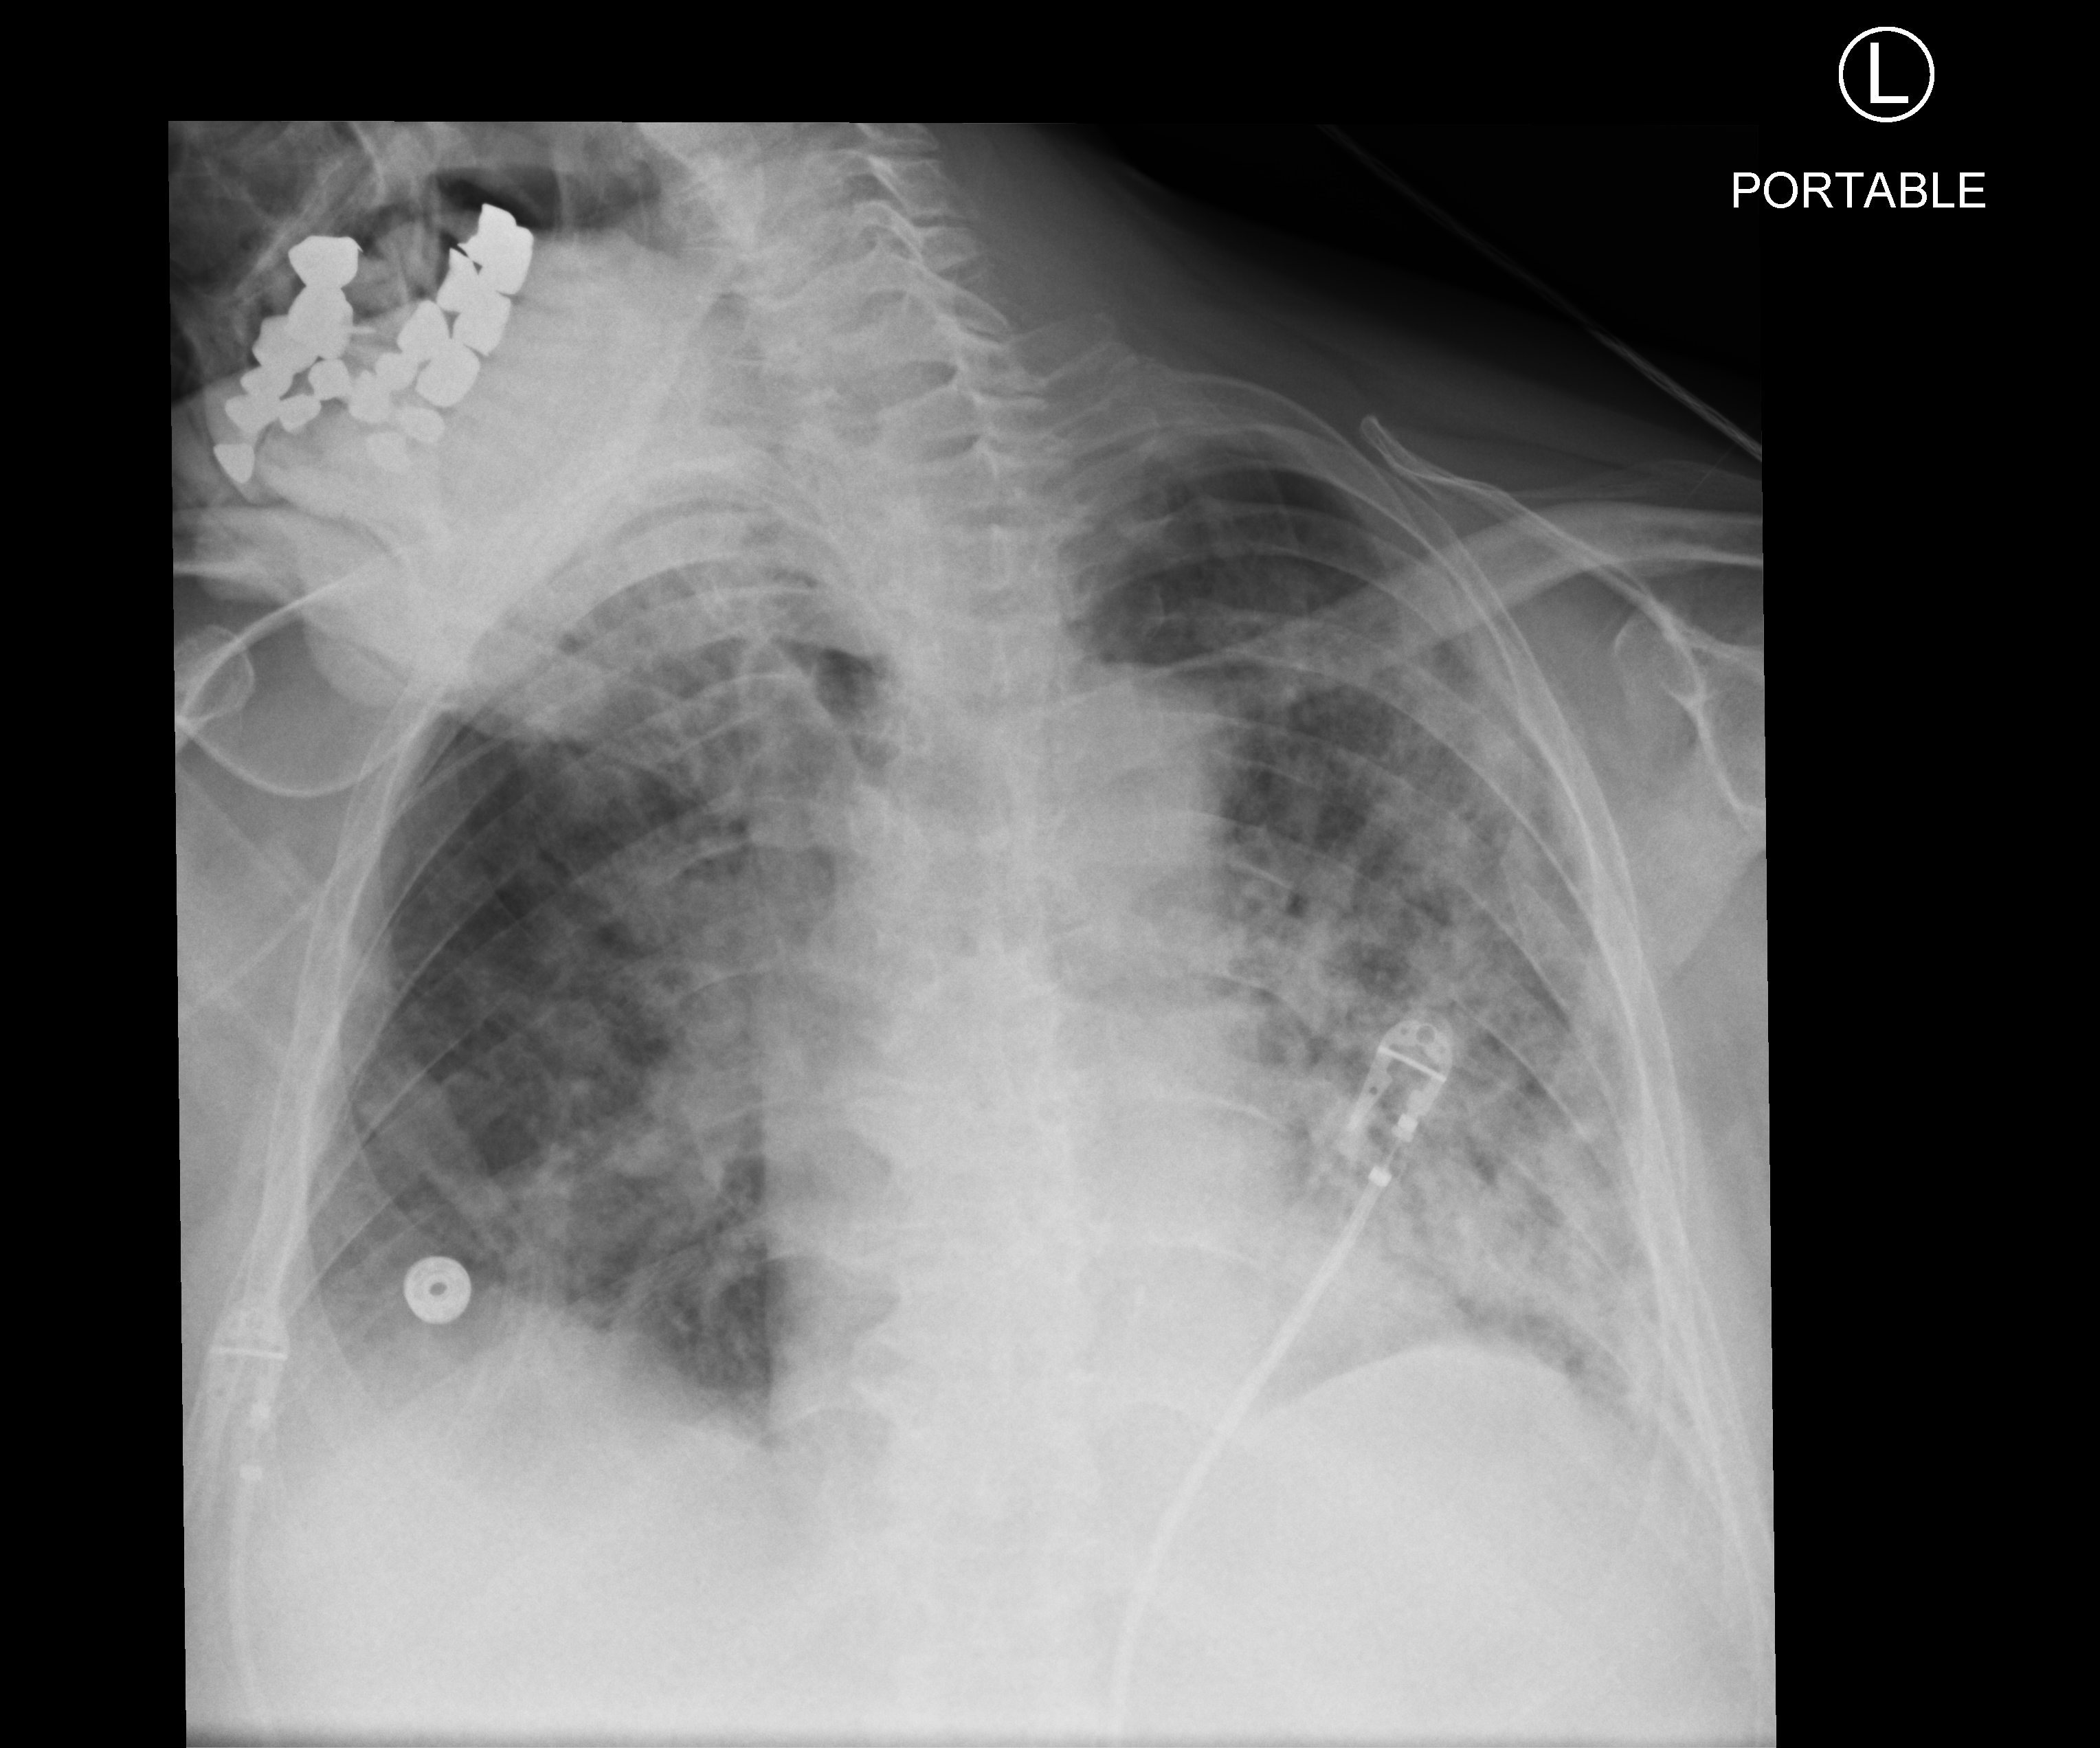
Bedside chest radiograph (computed radiography); anteroposterior (AP) projection. Patient hospitalised with COVID-19; male, aged 60–74 years.
From the hospital-stay record, not from the radiograph (when in the stay this image was taken is not recorded):
- admitted to intensive care during this hospital stay: yes